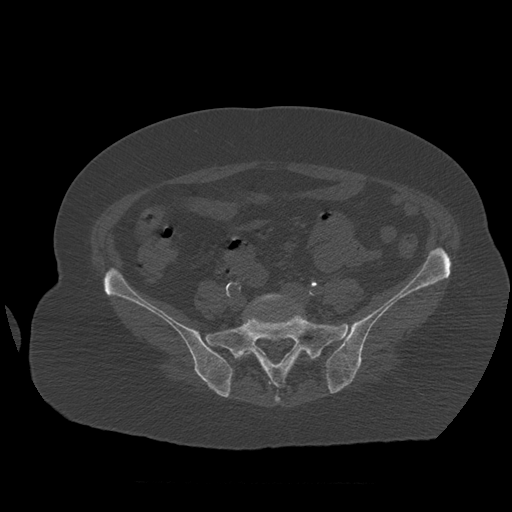
CT including the spine, one axial slice; position 168 of 399 along the scan axis; reconstruction kernel STANDARD; 120 kVp; bone window (W 1800 / L 400 HU); 1.25 mm slice thickness; 512 × 512 image matrix. Patient age 81 years. From the clinical record (not read from this slice): primary cancer: renal; vertebrae with lytic lesions (as recorded): L1.
Outlined on this slice (semi-automatic segmentation, software-assisted and operator-edited):
- L5 vertebra: bounding box <250,294,291,353> (left, top, right, bottom; pixels)